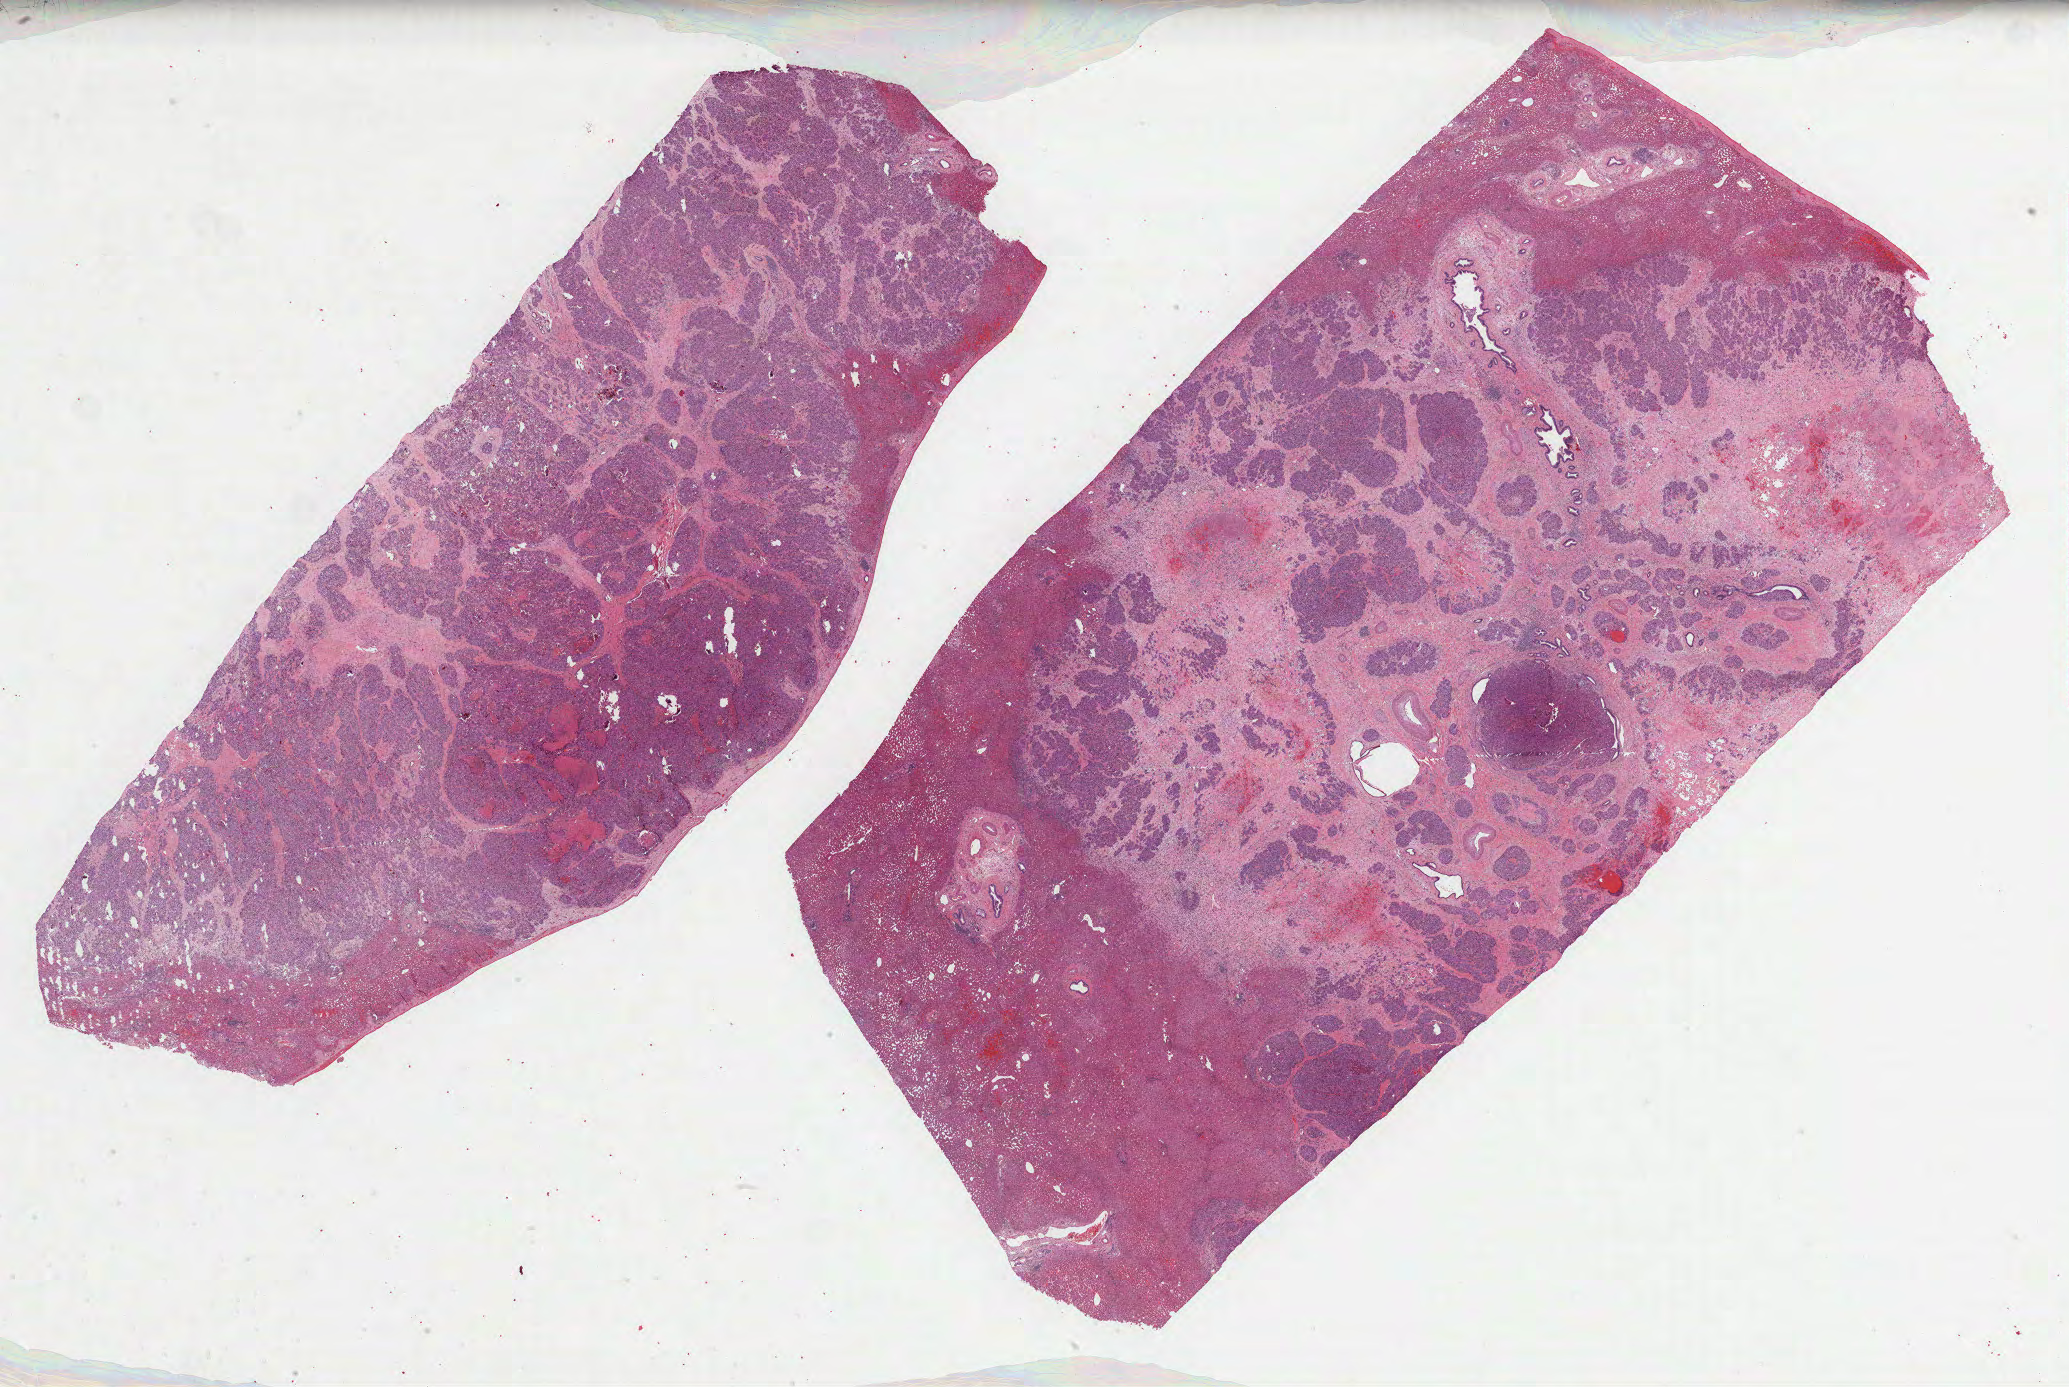
Digitized H&E tissue section (whole slide), a low-resolution overview of the entire scanned area, about 33.4 x 22.4 mm. Formalin-fixed paraffin-embedded (FFPE) diagnostic section. Sample: primary tumour, liver. Female patient; age at initial diagnosis 64 years. Histologic grade: G3 (poorly differentiated).
* TNM: T1 N0 MX
* AJCC pathologic stage: I (7th edition)
* diagnosis: Hepatocellular carcinoma, NOS